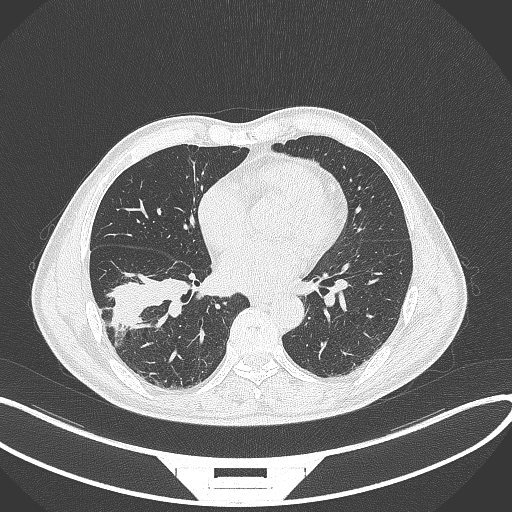
Chest CT, one axial slice. Position 156 of 364 along the scan axis. 120 kVp. Lung window (W 1500 / L -600 HU). 1 mm slice thickness. 512 × 512 image matrix. Male patient, age 58 years. From the clinical record (not read from this slice): clinical TNM (as recorded): T3 N0 M0; histopathological grade: G2.
Structures marked on this image (rectangle marked by the reading radiologist):
- lung tumour (recorded histology: squamous cell carcinoma): box from (x=108, y=273) to (x=192, y=337) px